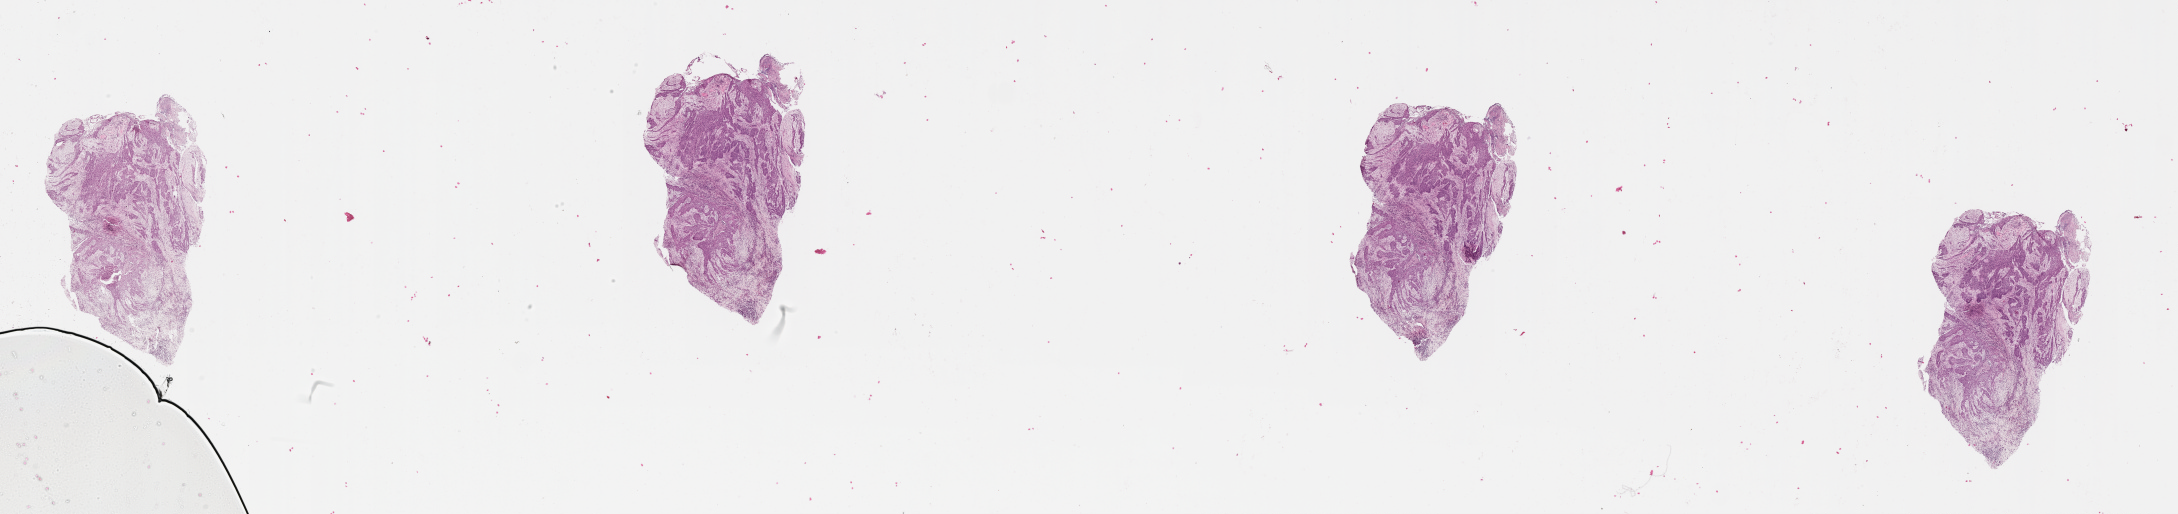
Digitized H&E-stained tissue section (whole slide) — a low-resolution overview of the entire scanned area, about 35.1 x 8.3 mm (acquisition: 20x scan). Tumour tissue sample, sampled site: floor of mouth. Patient: male, age 71 years. Histologic grade: G2 (moderately differentiated). Composition of this section per pathologist review: tumour nuclei 80%, necrosis 5%.
- primary tumour site (as recorded): oral cavity
- diagnosis: Squamous cell carcinoma, NOS (floor of mouth, NOS)
- AJCC pathologic stage: II